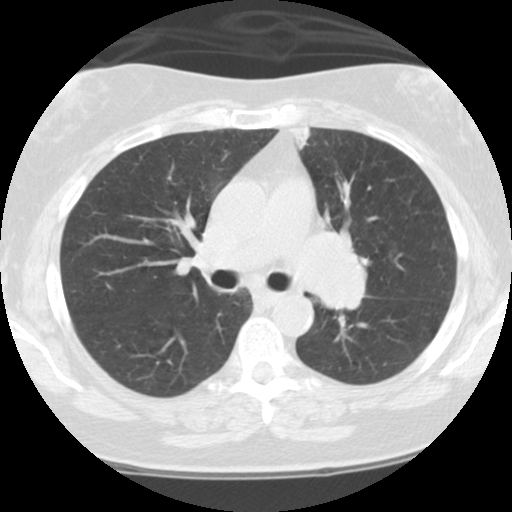
Chest CT (low-dose screening protocol), one axial image, third screening round (two years after baseline), lung window (W 1500 / L -600 HU), 2.5 mm slice thickness, slice 41 of 108 in the series. Female participant, aged 59 years at enrolment. Current smoker at enrolment.
Lesion marked by an expert reader, box from (x=285, y=213) to (x=384, y=325) px. No non-calcified nodule or mass ≥4 mm was recorded by the screening reader at this exam. Official screen result: positive, other.